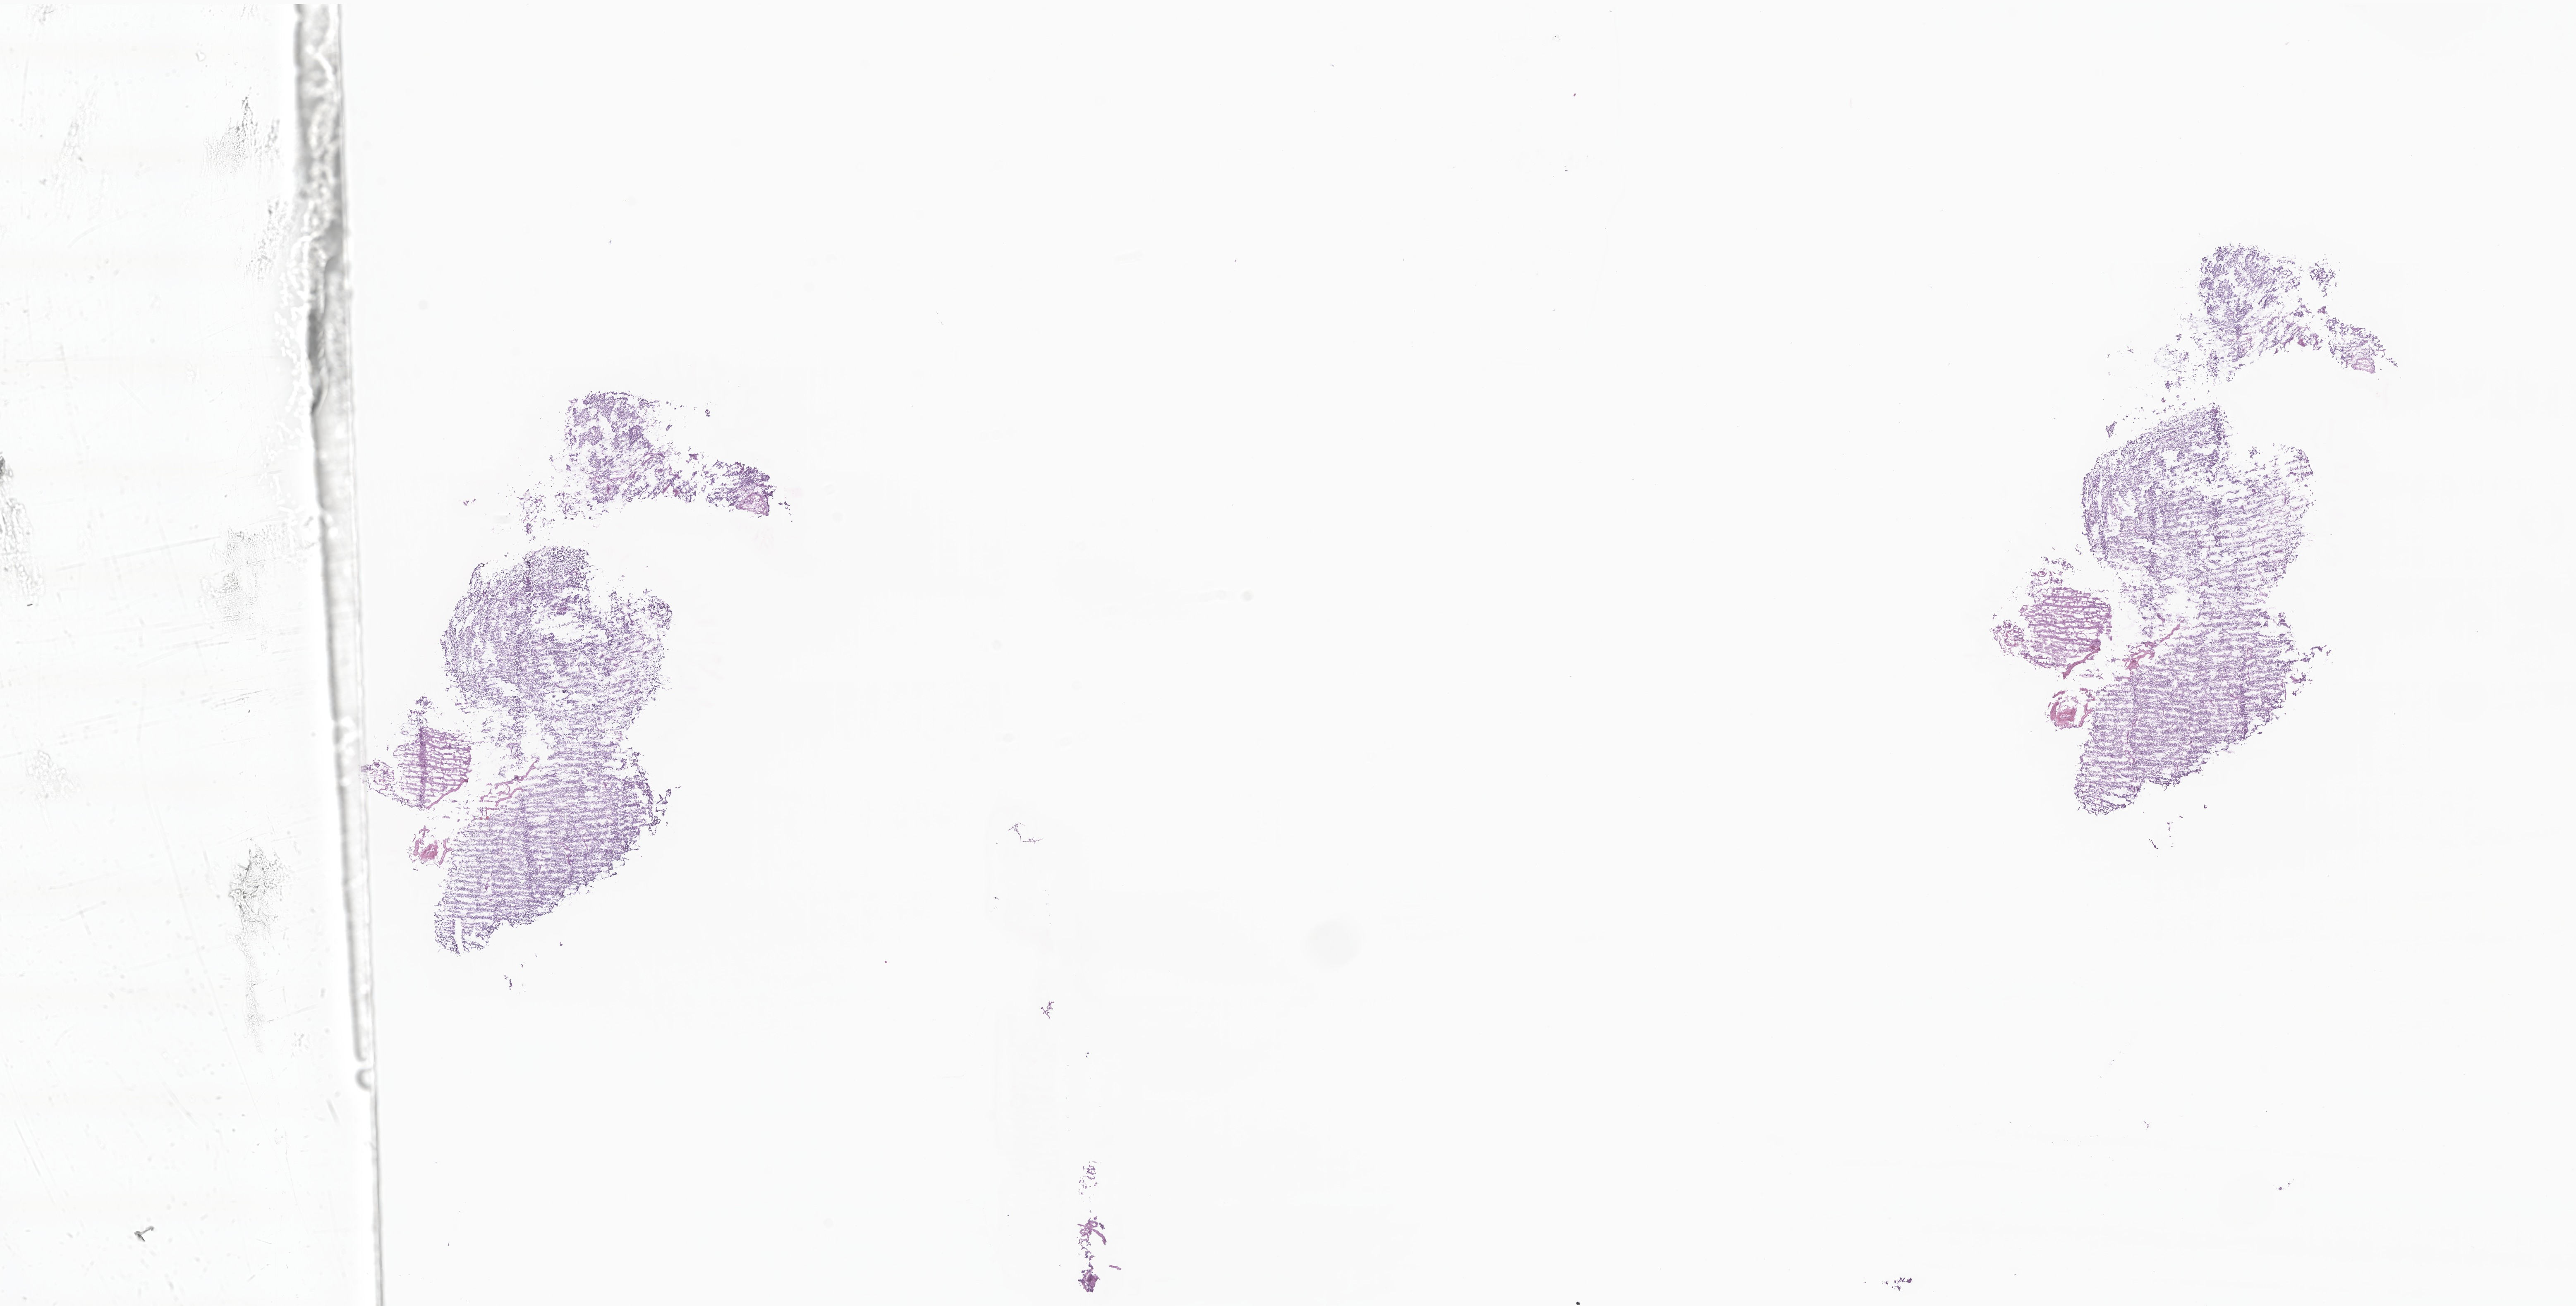
Digitized H&E-stained section of tumor tissue from the brain — low-resolution overview of the scanned area, about 26.3 x 13.3 mm; frozen section (OCT-embedded). Male patient, age 232 months.
Diagnosis (ICD-O-3 morphology term): Neoplasm, malignant.